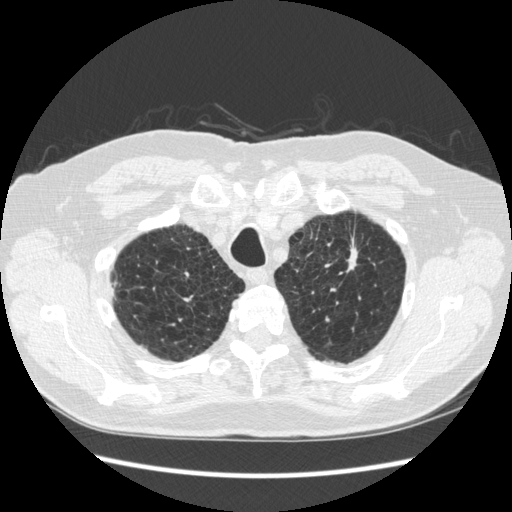
Low-dose screening chest CT, one axial slice; slice 229 of 267 in the series (ordered by position); 120 kVp; lung window (W 1500 / L -600 HU); 1.25 mm slice thickness; 512 × 512 image matrix, field of view 360 × 360 mm.
Structures marked on this image (manually delineated by an expert):
- lesion 1 (tumor, upper lobe of left lung): bounding box <348,244,358,270> (left, top, right, bottom; pixels)